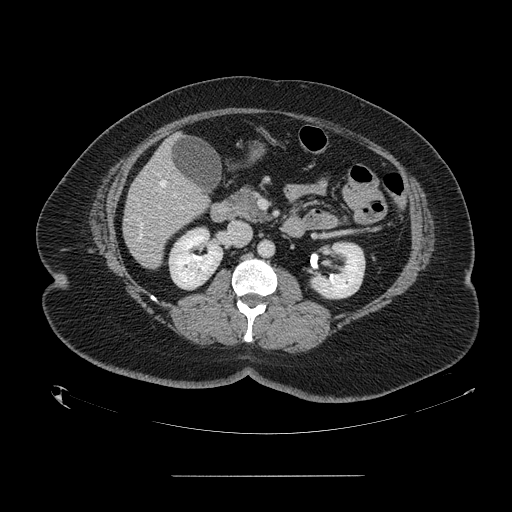
Contrast-enhanced abdominal CT, one axial slice. Slice 61 of 164 in the series (ordered by position). Intravenous contrast given. Soft-tissue window (W 400 / L 40 HU). 2.5 mm slice thickness. 512 × 512 image matrix, field of view 495 × 495 mm. Female patient, age 52 years. From the clinical record (not read from this slice): diagnosis: colorectal cancer liver metastases, imaged before liver resection; multiple liver metastases: yes; largest metastasis: 3.5 cm; disease in both lobes: no.
Structures marked on this image (outlined manually by an expert reader):
- hepatic veins: bounding box (x1, y1, x2, y2) in pixels: (137, 180, 166, 242)
- liver: (124, 140, 208, 268)
- portal vein (with intrahepatic branches): (173, 194, 176, 197)